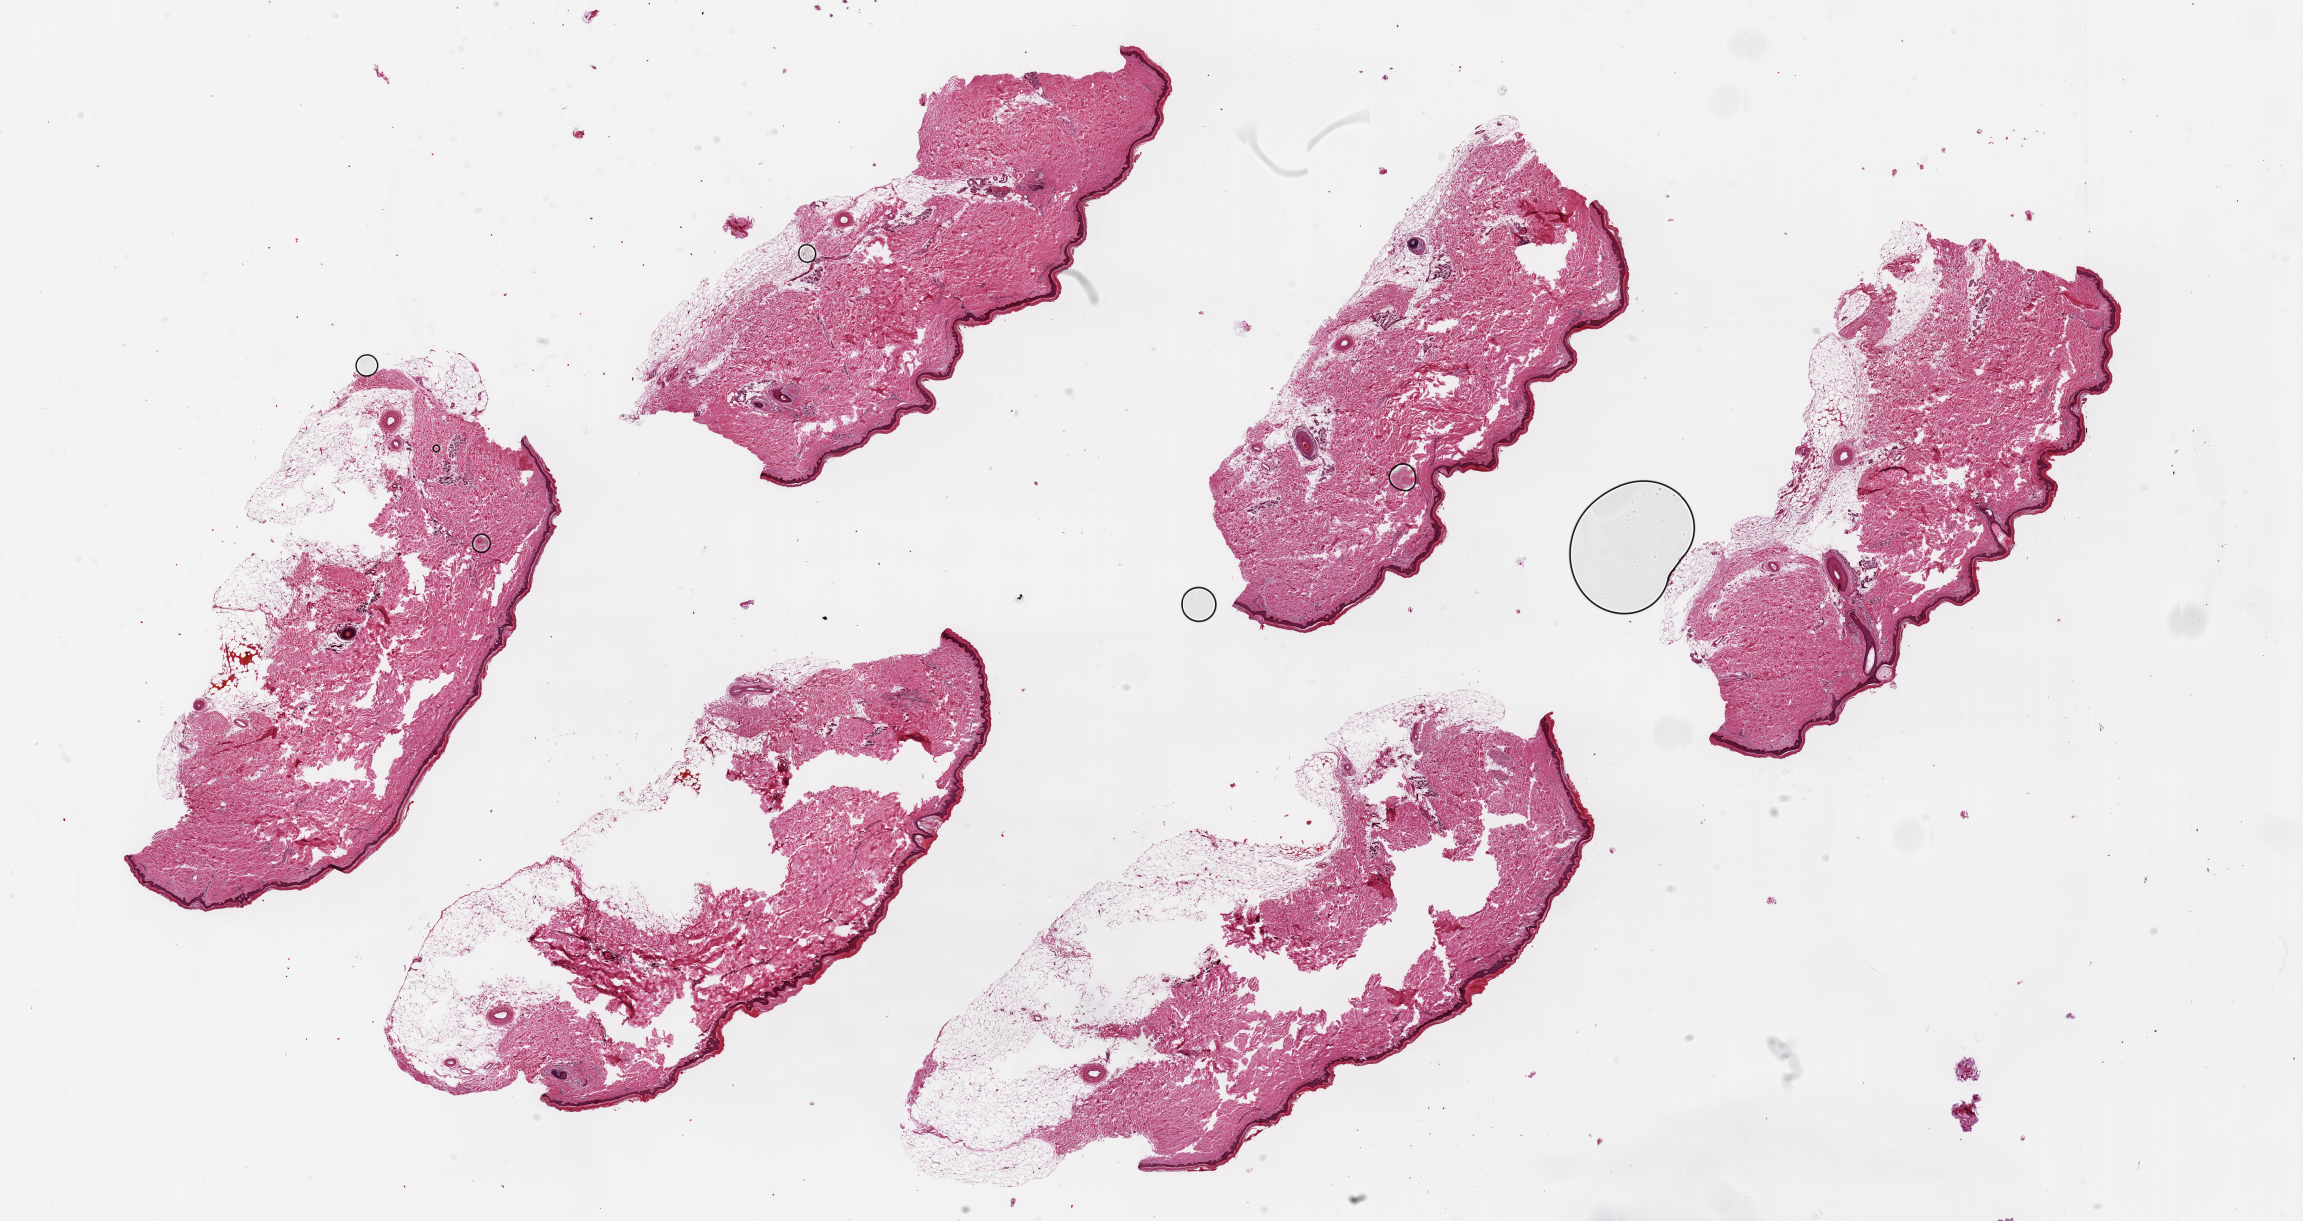
Hematoxylin and eosin (H&E) whole-slide image, brightfield — shown as a low-resolution overview of the whole scanned area (about 36.4 x 19.3 mm, acquisition: 20x scan), PAXgene-fixed, paraffin-embedded tissue, section of skin of lower leg (target tissue), donor tissue sample.
Reviewer comment on this tissue sample: 6 pieces, up to 9x4.5mm; up to 2 mm thick subcutaneous adipose in 5 pieces.